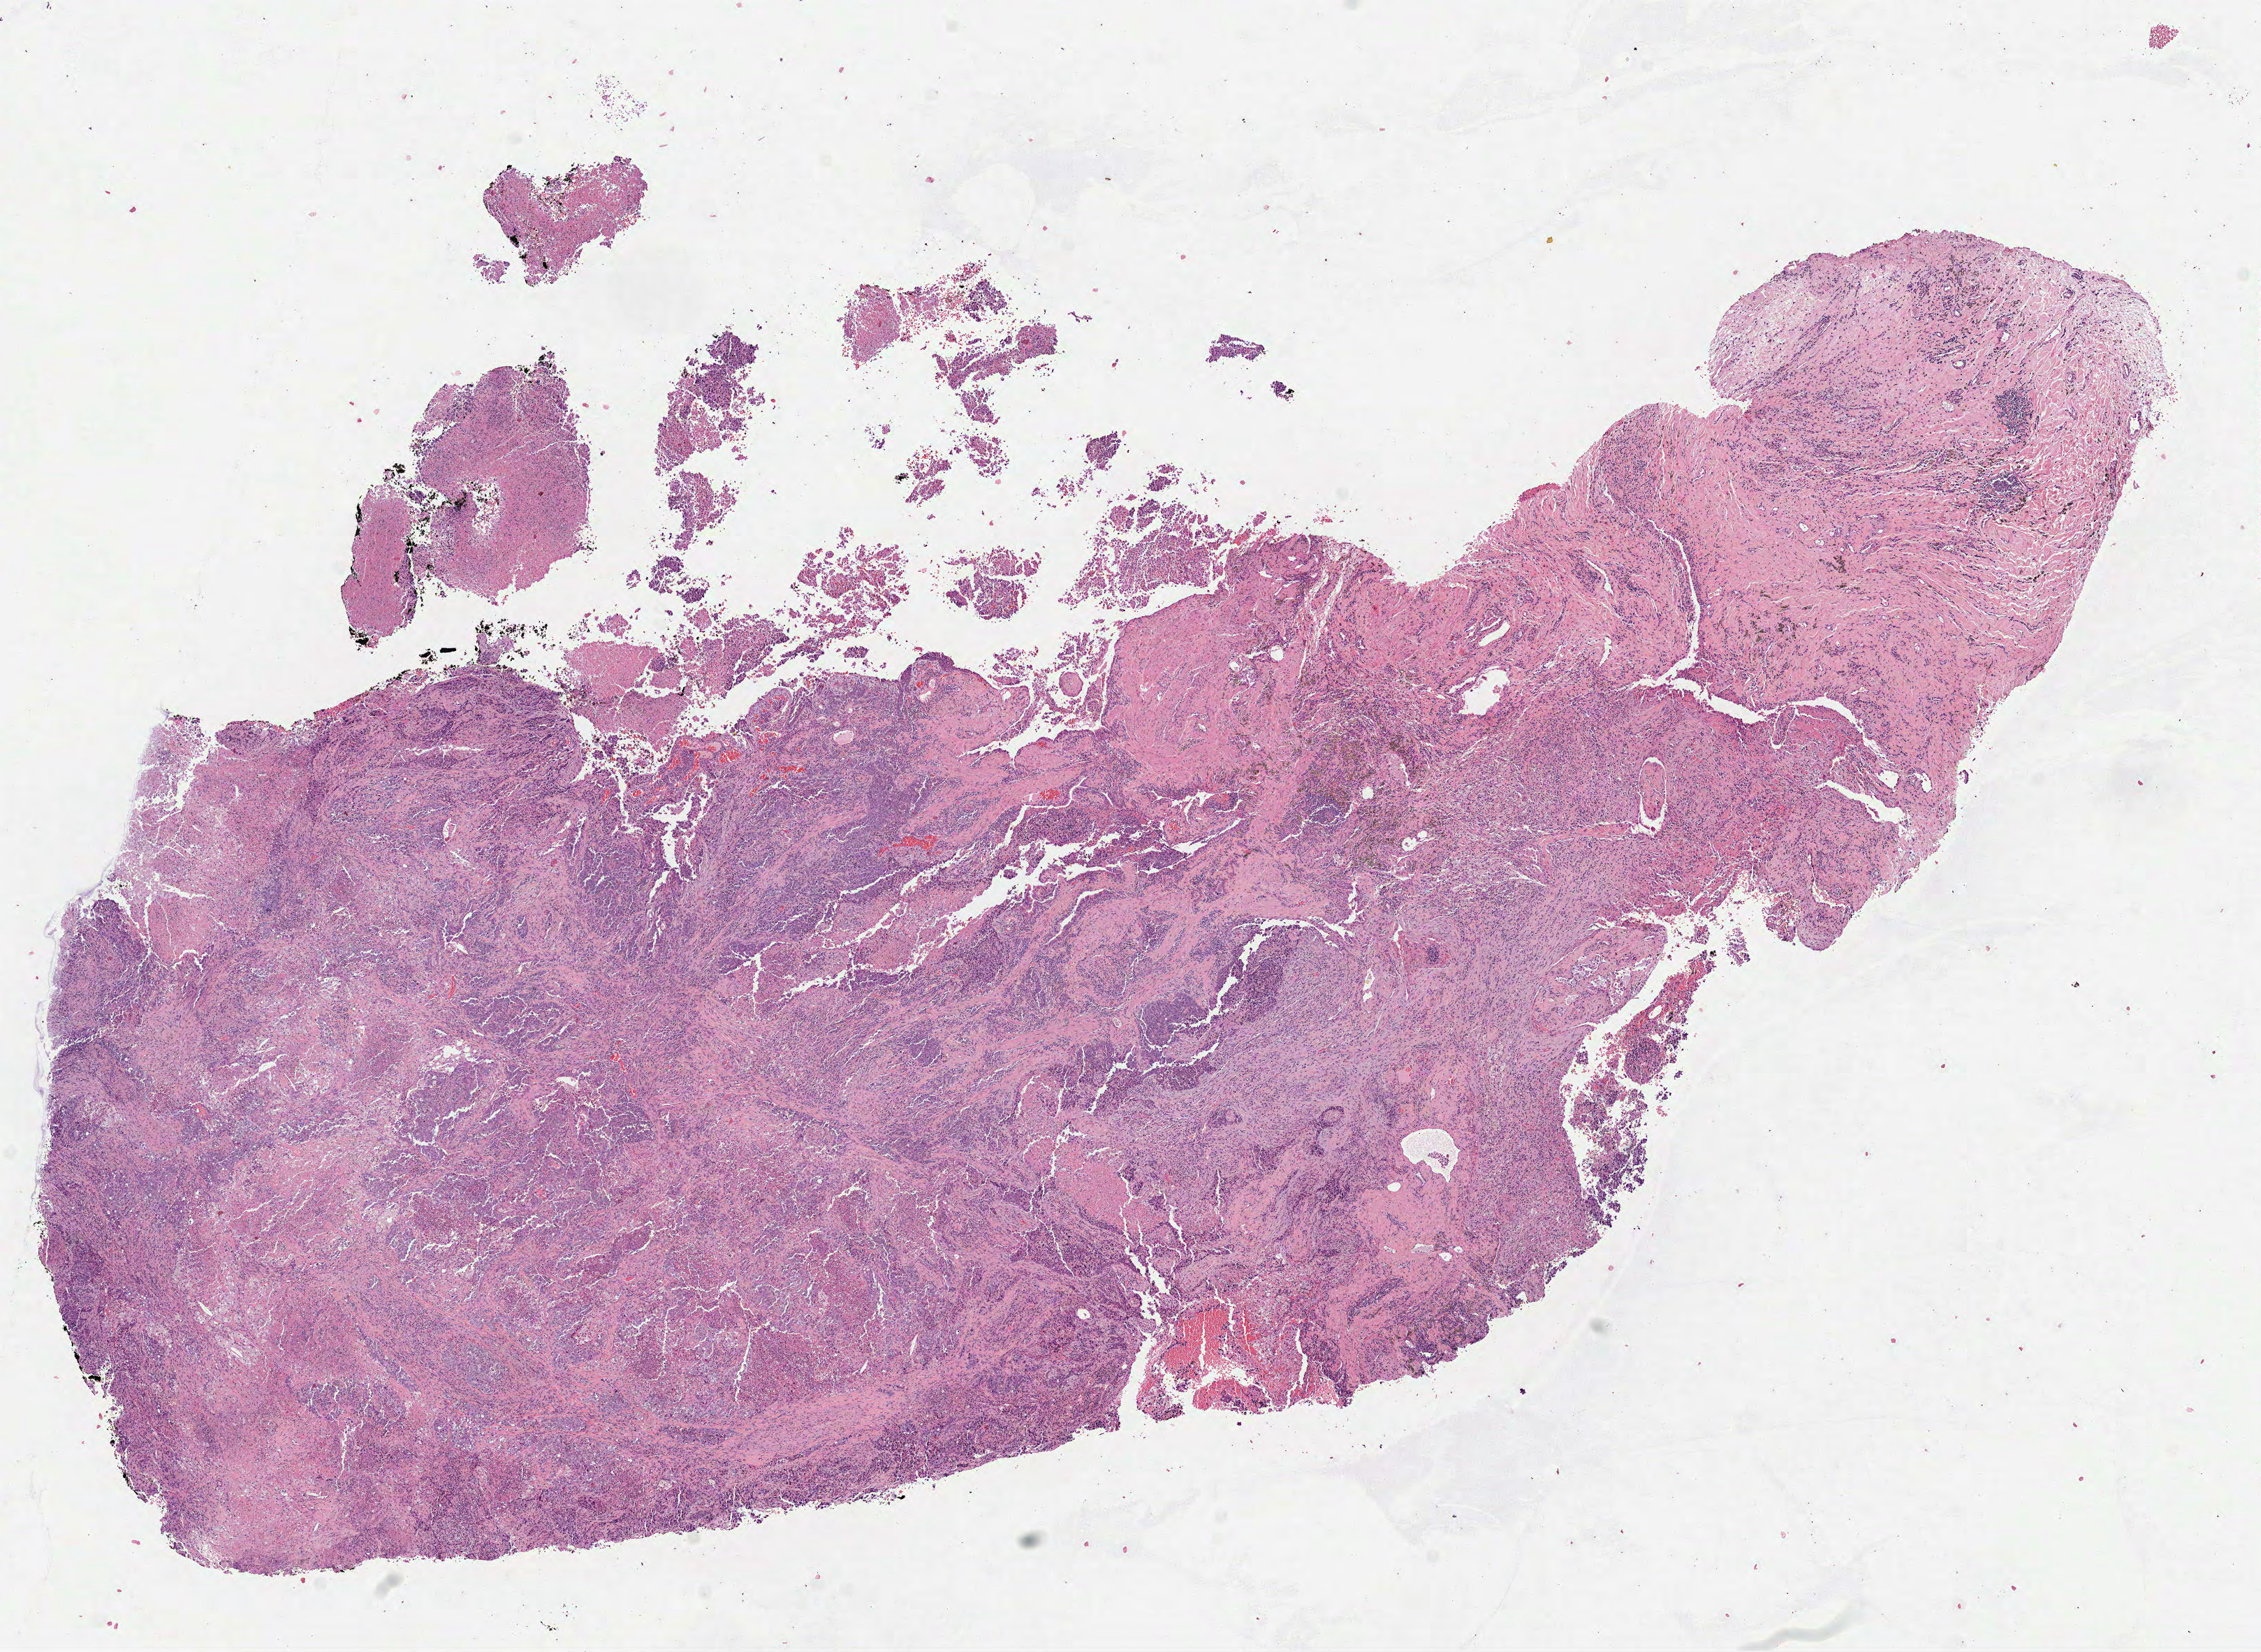
H&E-stained whole-slide image — a low-resolution overview of the entire scanned area, about 13.1 x 9.5 mm; FFPE section; sample: primary tumour, lung. Male, age 67 years at initial diagnosis.
Histologic diagnosis: Squamous cell carcinoma, NOS (upper lobe, lung).